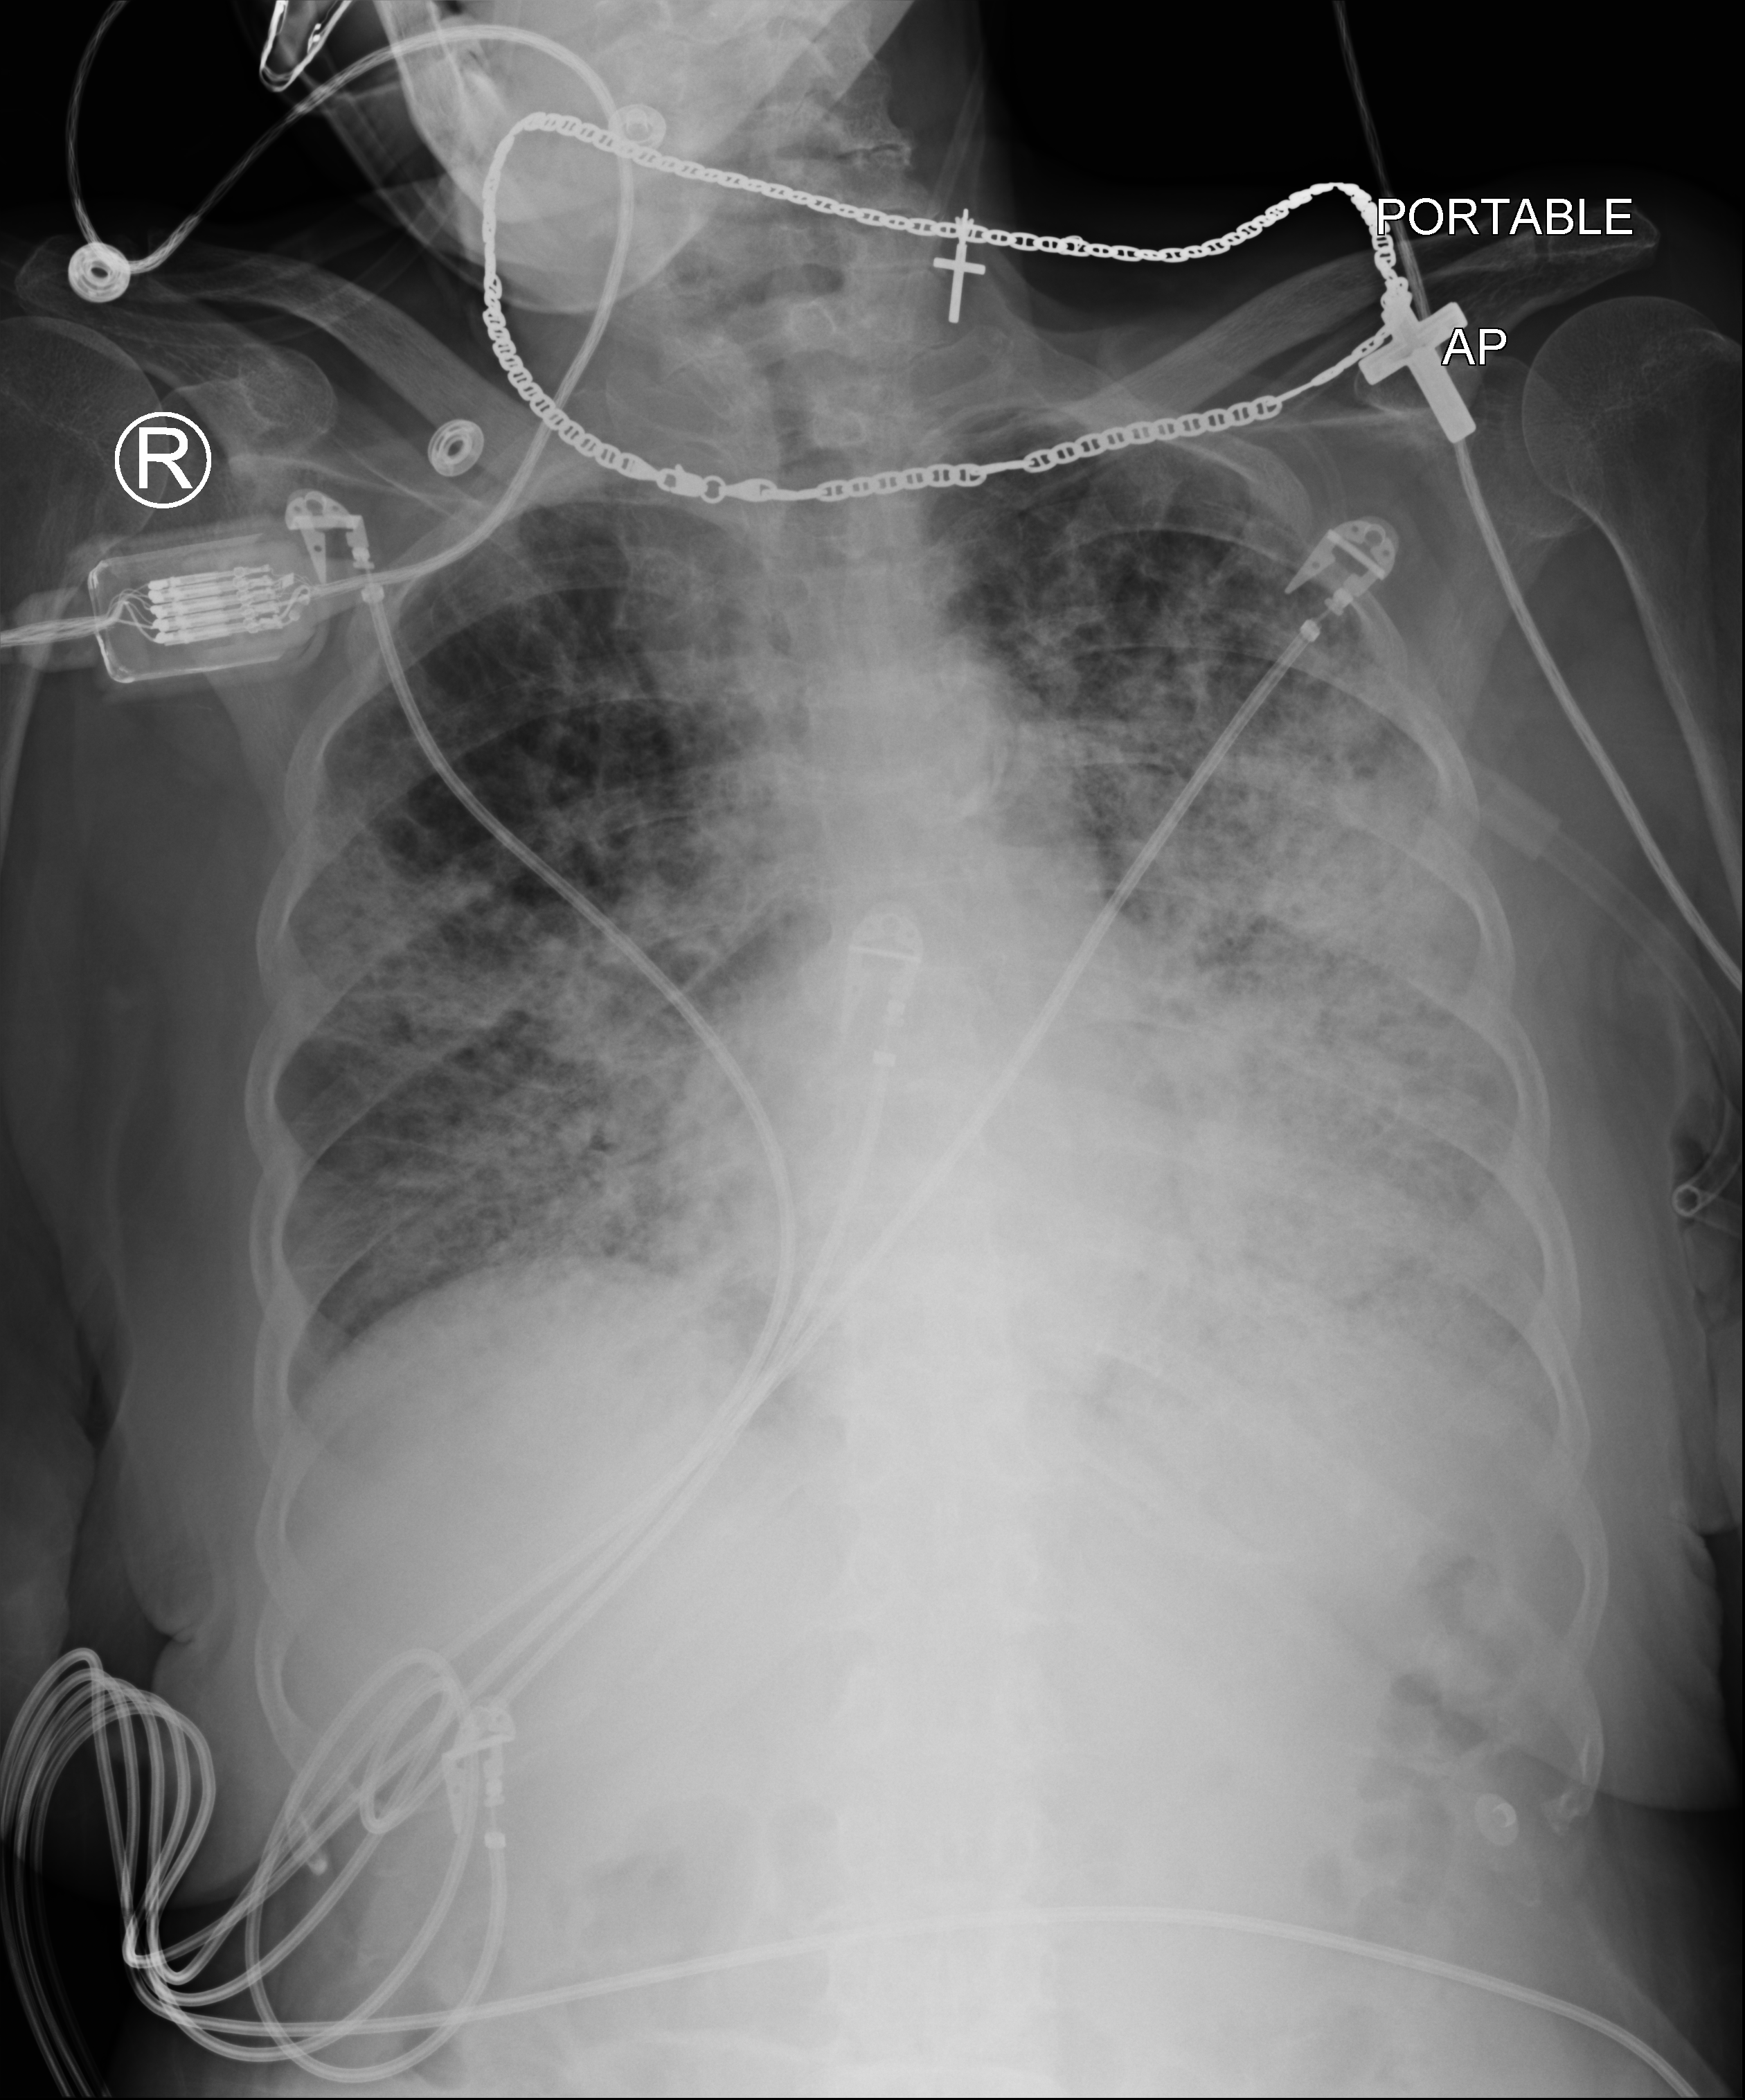
Bedside chest radiograph (computed radiography); anteroposterior (AP) projection. Patient hospitalised with COVID-19; female, aged 75–90 years.
Admission-level facts for this patient (not findings on this image; timing relative to this image not recorded):
- admitted to intensive care during this hospital stay: no